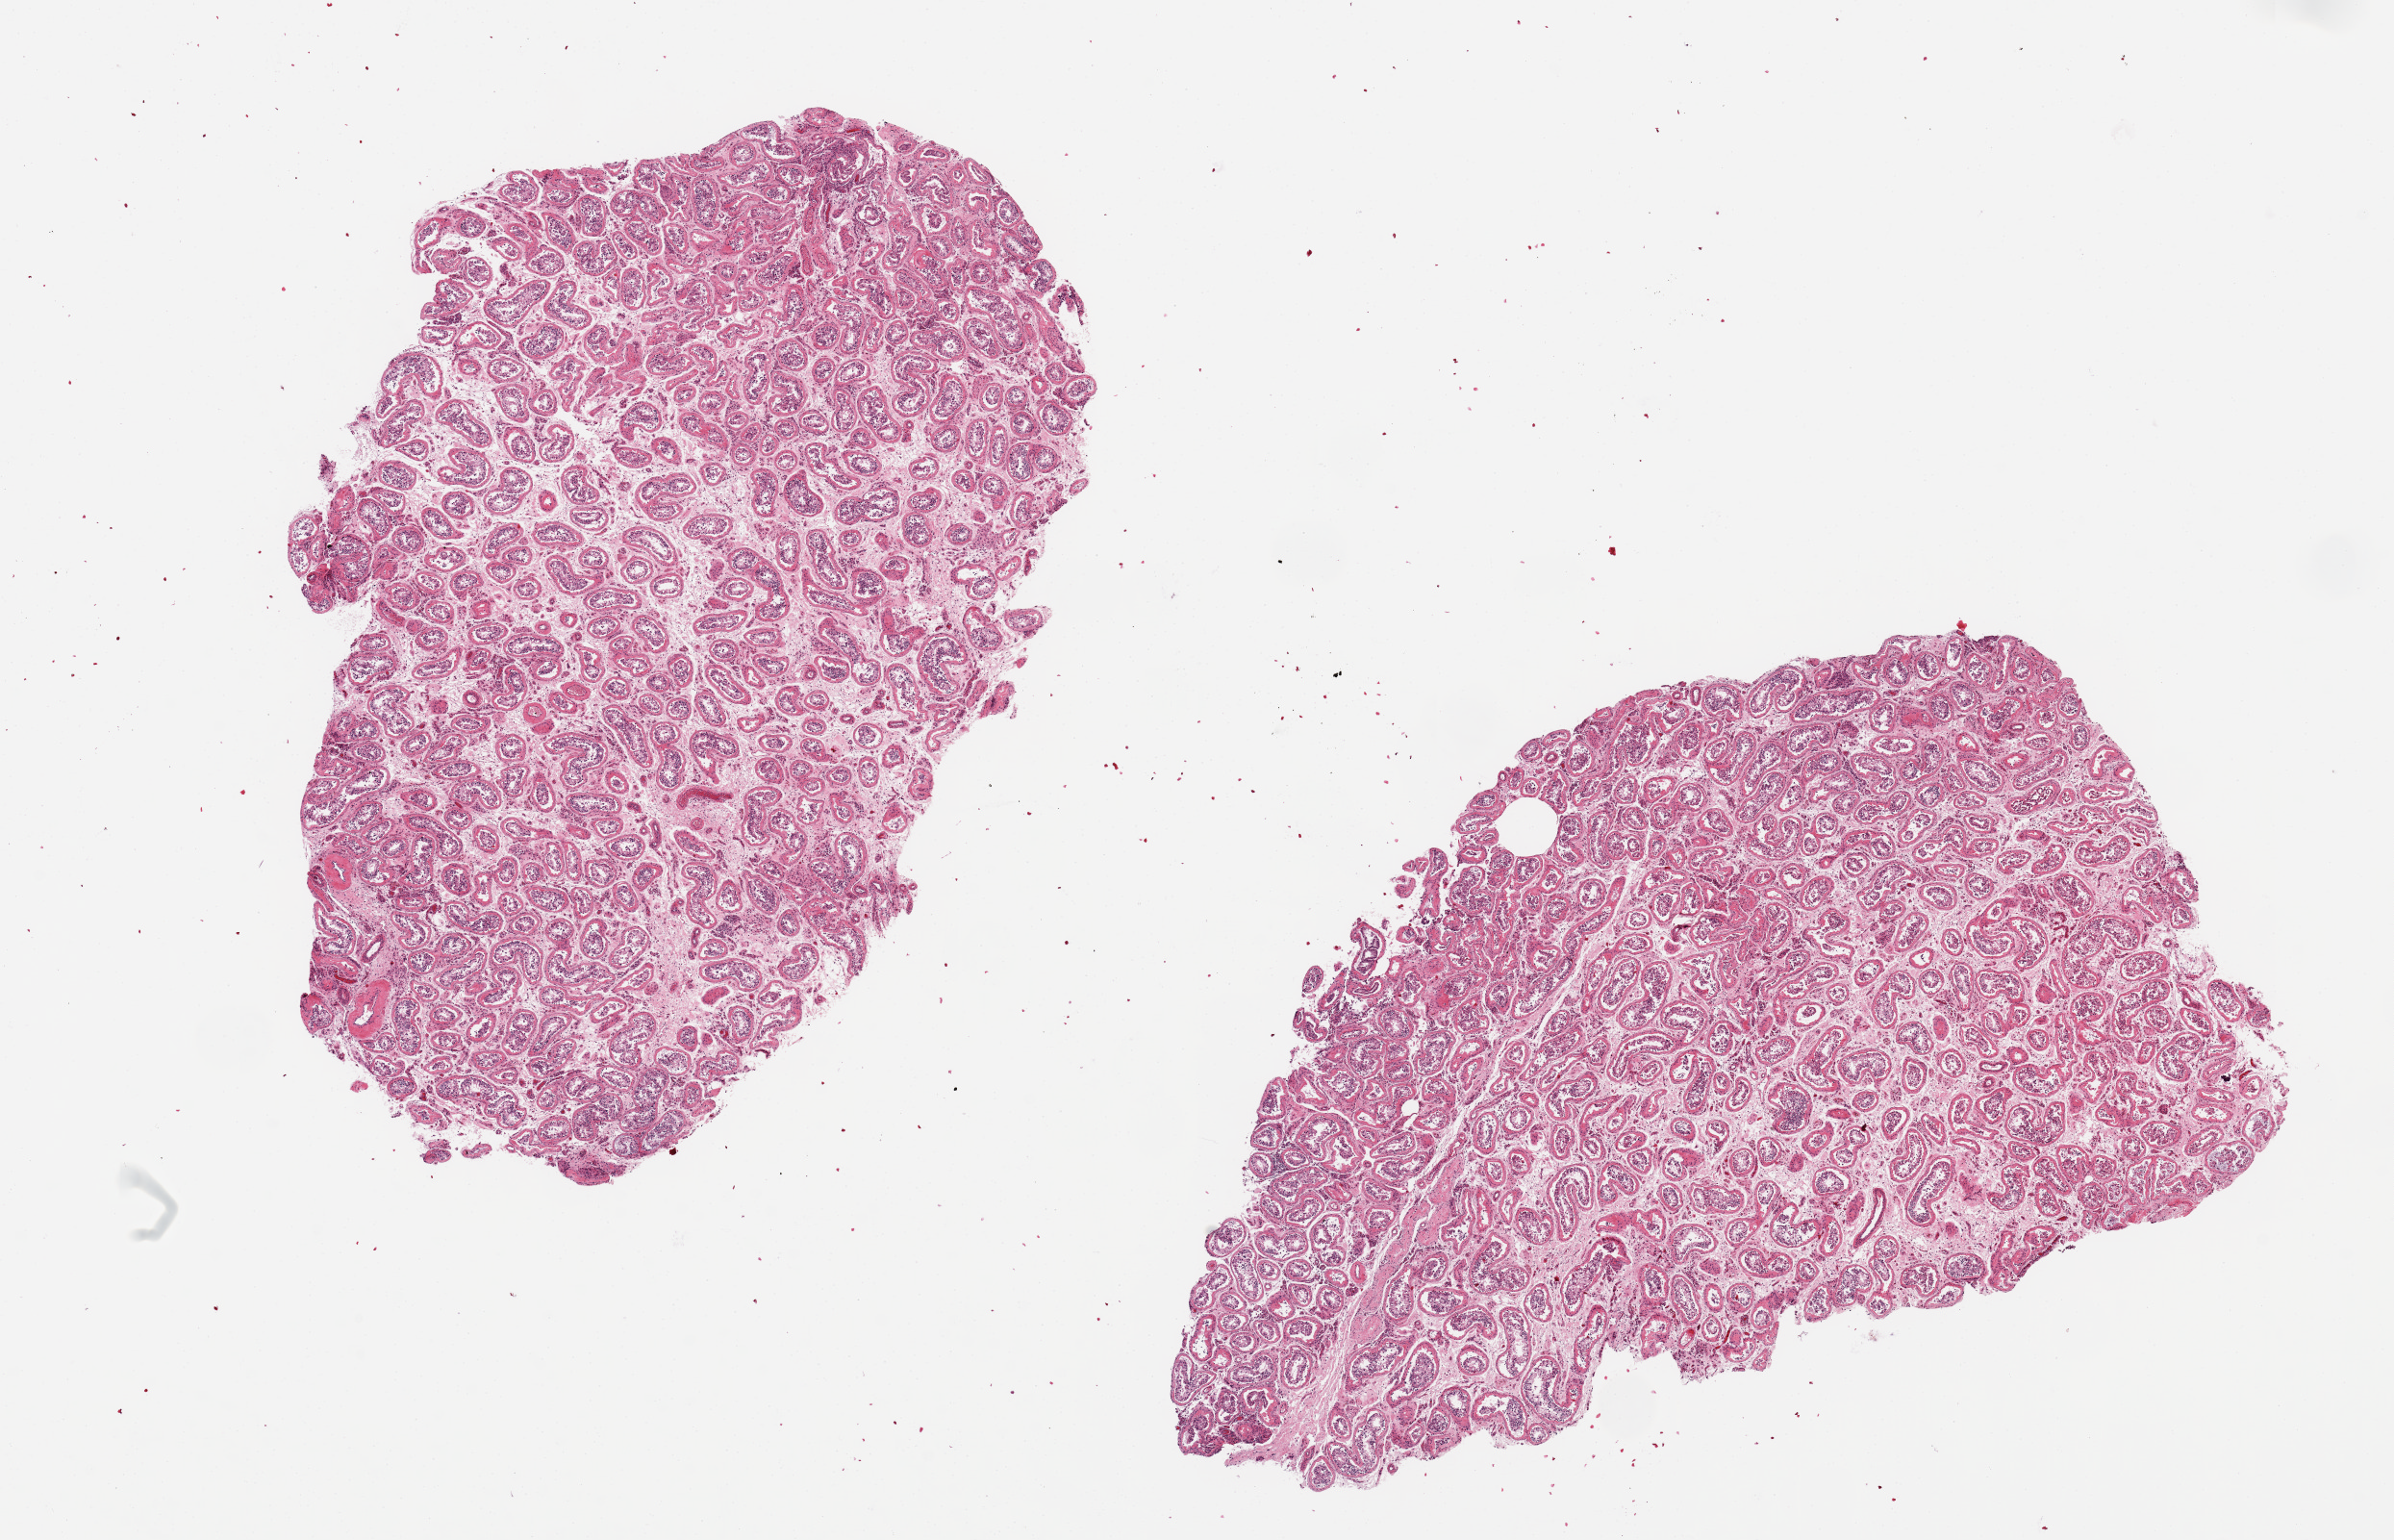
H&E whole-slide image — low-resolution overview of the scanned area, about 19.7 x 12.7 mm; PAXgene-fixed, paraffin-embedded tissue; section of testis (target tissue); donor tissue sample. Donor: male.
Pathologist's review note for this sample: 2, 9x5 mm pieces; reduced spermatogenesis.